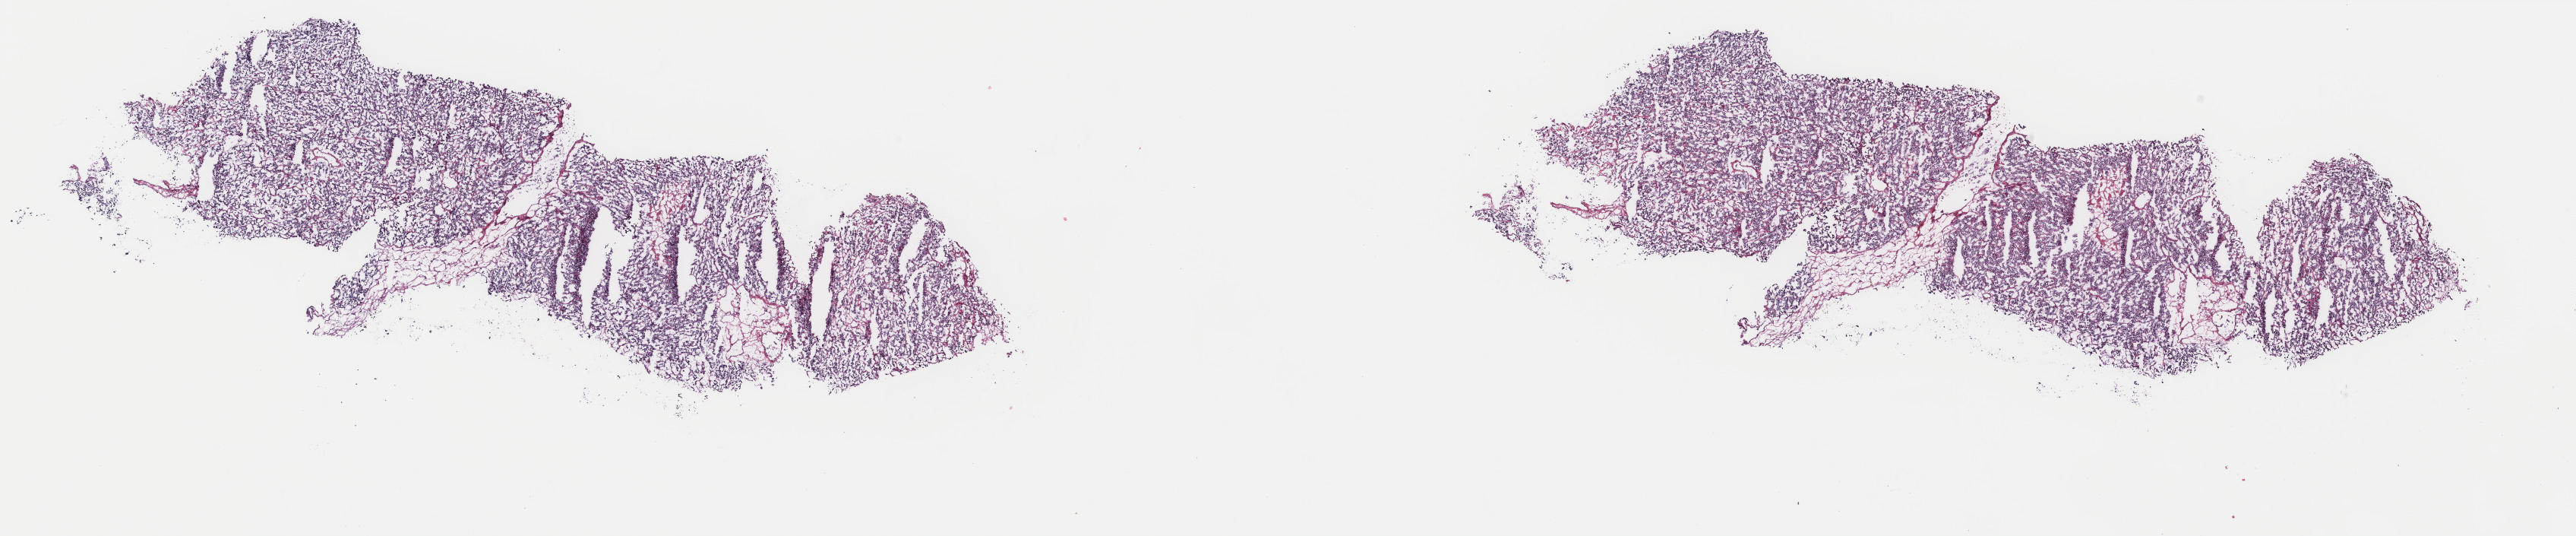
Hematoxylin and eosin (H&E) stained whole-slide image — whole scanned area (about 26.9 x 5.6 mm, slide scanned at 40x) shown as a low-resolution overview, frozen section from the top of the tissue portion, primary tumour sample from the adrenal gland. Female, age 54 years at initial diagnosis. Slide review estimates, as recorded: tumour cells 95%, tumour nuclei 95%, normal cells 0%, stromal cells 5%, necrosis 0%. Infiltration values recorded for this section: lymphocyte infiltration 0%, monocyte infiltration 0%, neutrophil infiltration 0%.
• pathologic diagnosis: Pheochromocytoma, NOS